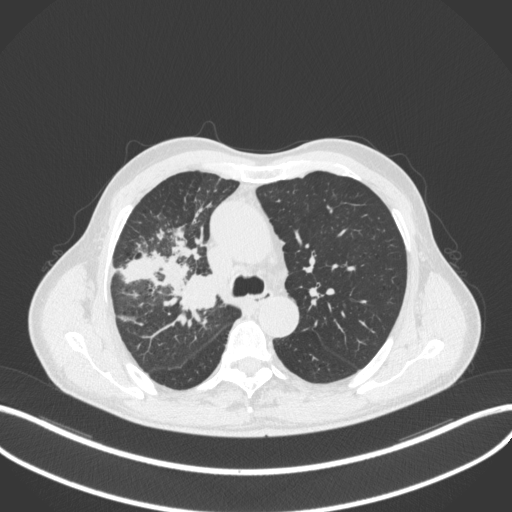
Chest CT, one axial slice; position 330 of 490 along the scan axis; reconstruction kernel B31f; 120 kVp; lung window (W 1500 / L -600 HU); 1 mm slice thickness; 512 × 512 image matrix, field of view 400 × 400 mm. Male patient, age 69 years. Case-level facts recorded for this patient, not image findings: clinical TNM (as recorded): T2a N0 M0.
Annotated regions visible in this slice (bounding box drawn by a radiologist):
- lung tumour (recorded histology: adenocarcinoma): bounding box (x1, y1, x2, y2) in pixels: (177, 272, 219, 309)